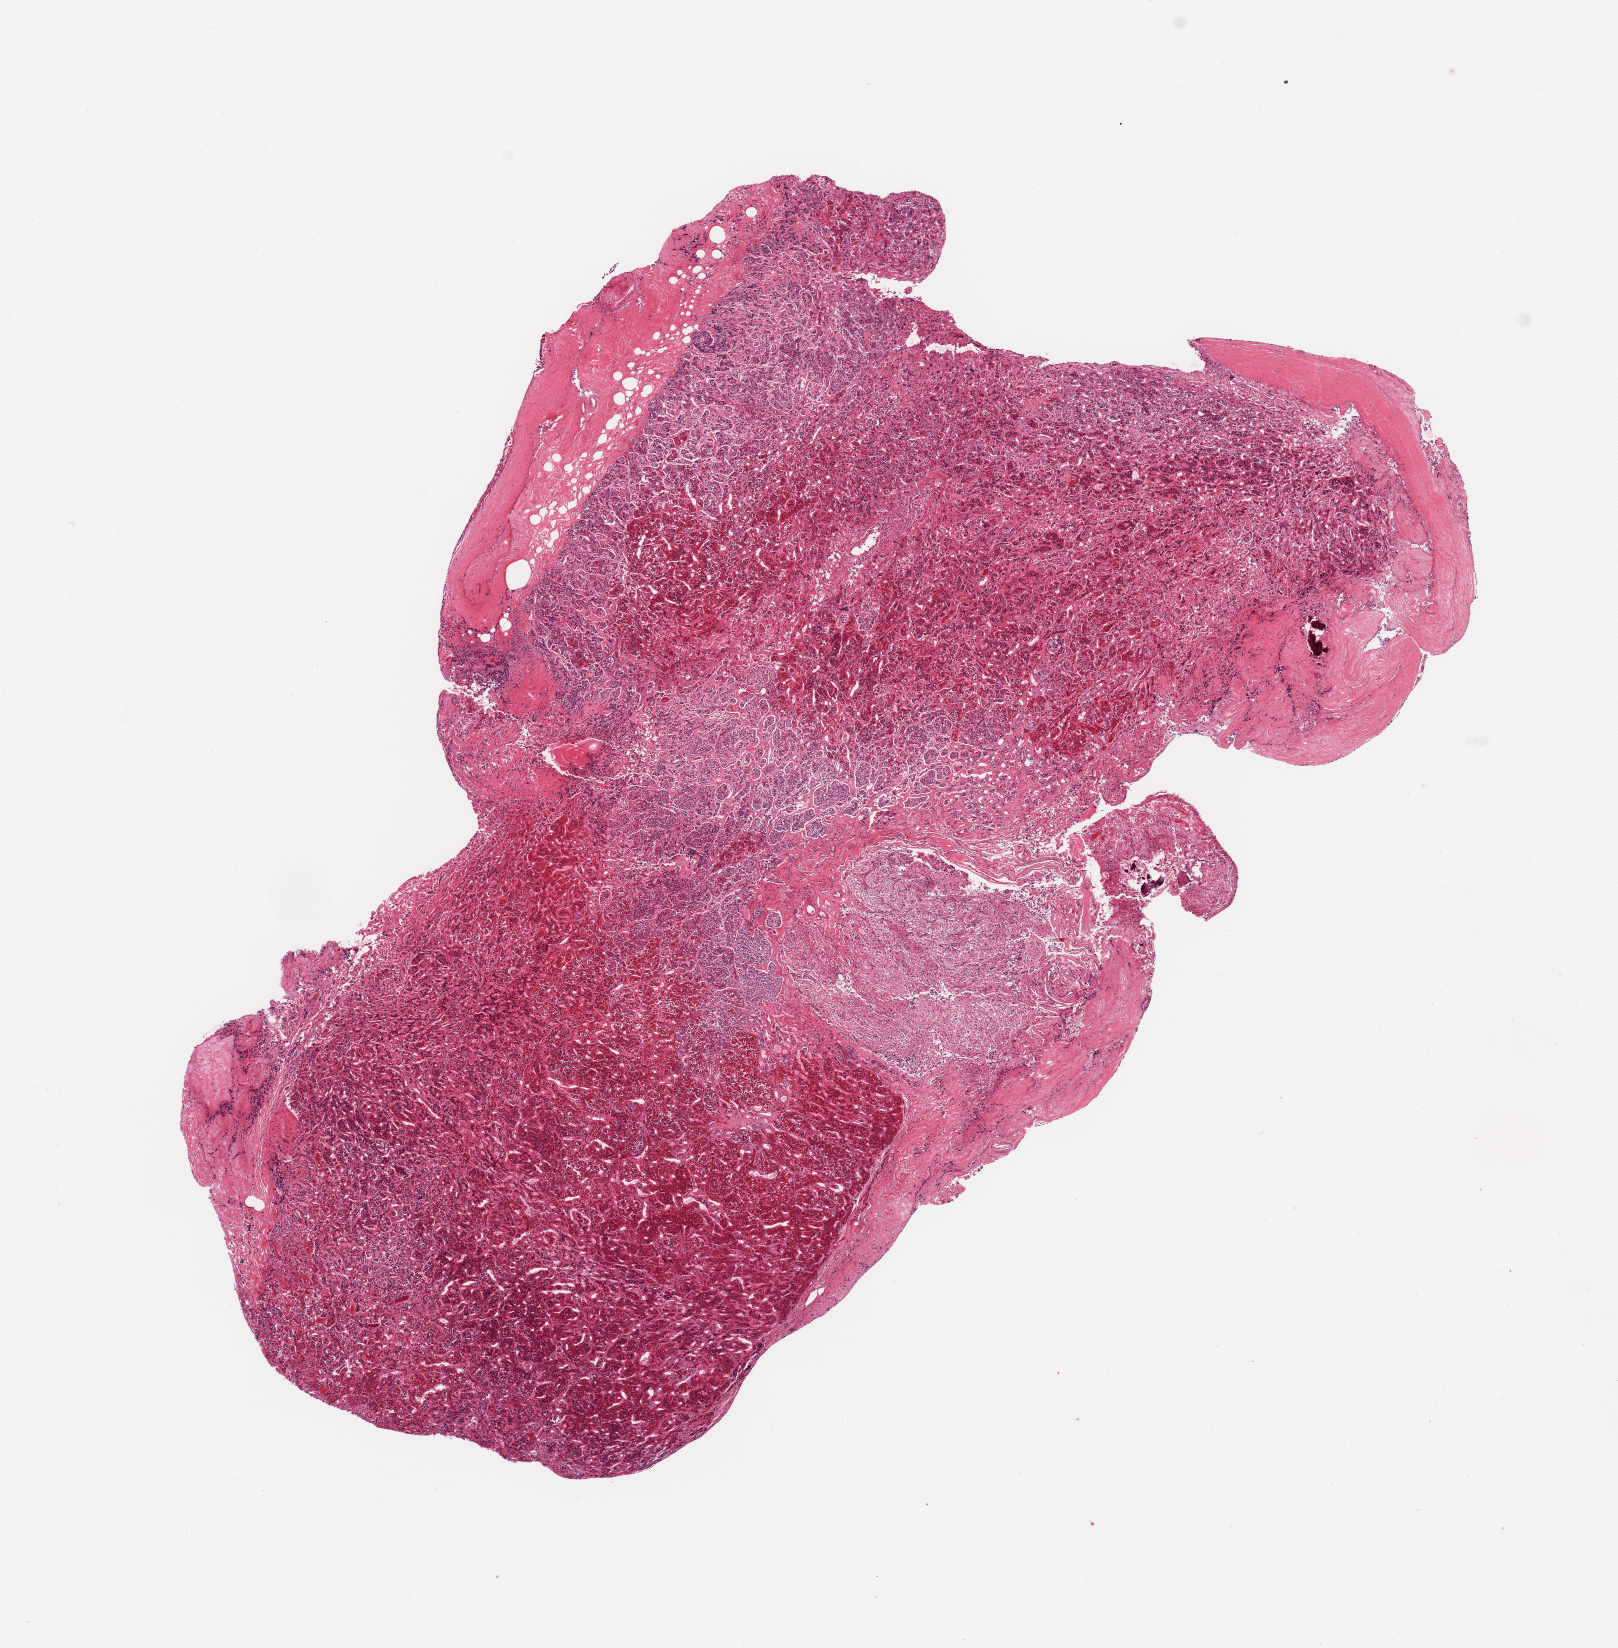
Hematoxylin and eosin (H&E) whole-slide image, a low-resolution overview of the entire scanned area, about 12.8 x 13.0 mm, PAXgene-fixed, paraffin-embedded tissue, section of pituitary (target tissue), donor tissue sample.
Reviewer comment on this tissue sample: 1 piece, mainly adenohypophysis; ~2mm nubbin of neurohypophysis.